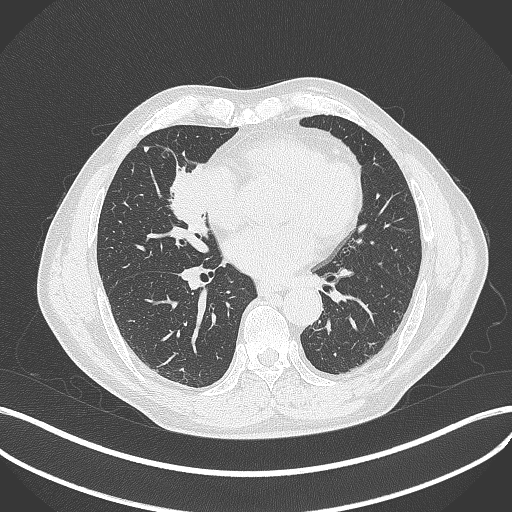
Chest CT, one axial slice; position 179 of 429 along the scan axis; reconstruction kernel B70f; 120 kVp; lung window (W 1500 / L -600 HU); 1 mm slice thickness; 512 × 512 image matrix, field of view 400 × 400 mm. Male patient, age 61 years. Case-level facts recorded for this patient, not image findings: clinical TNM (as recorded): T2b N1 M0.
Annotated regions visible in this slice (bounding box drawn by a radiologist):
- lung tumour (recorded histology: squamous cell carcinoma): box from (x=165, y=157) to (x=214, y=240) px